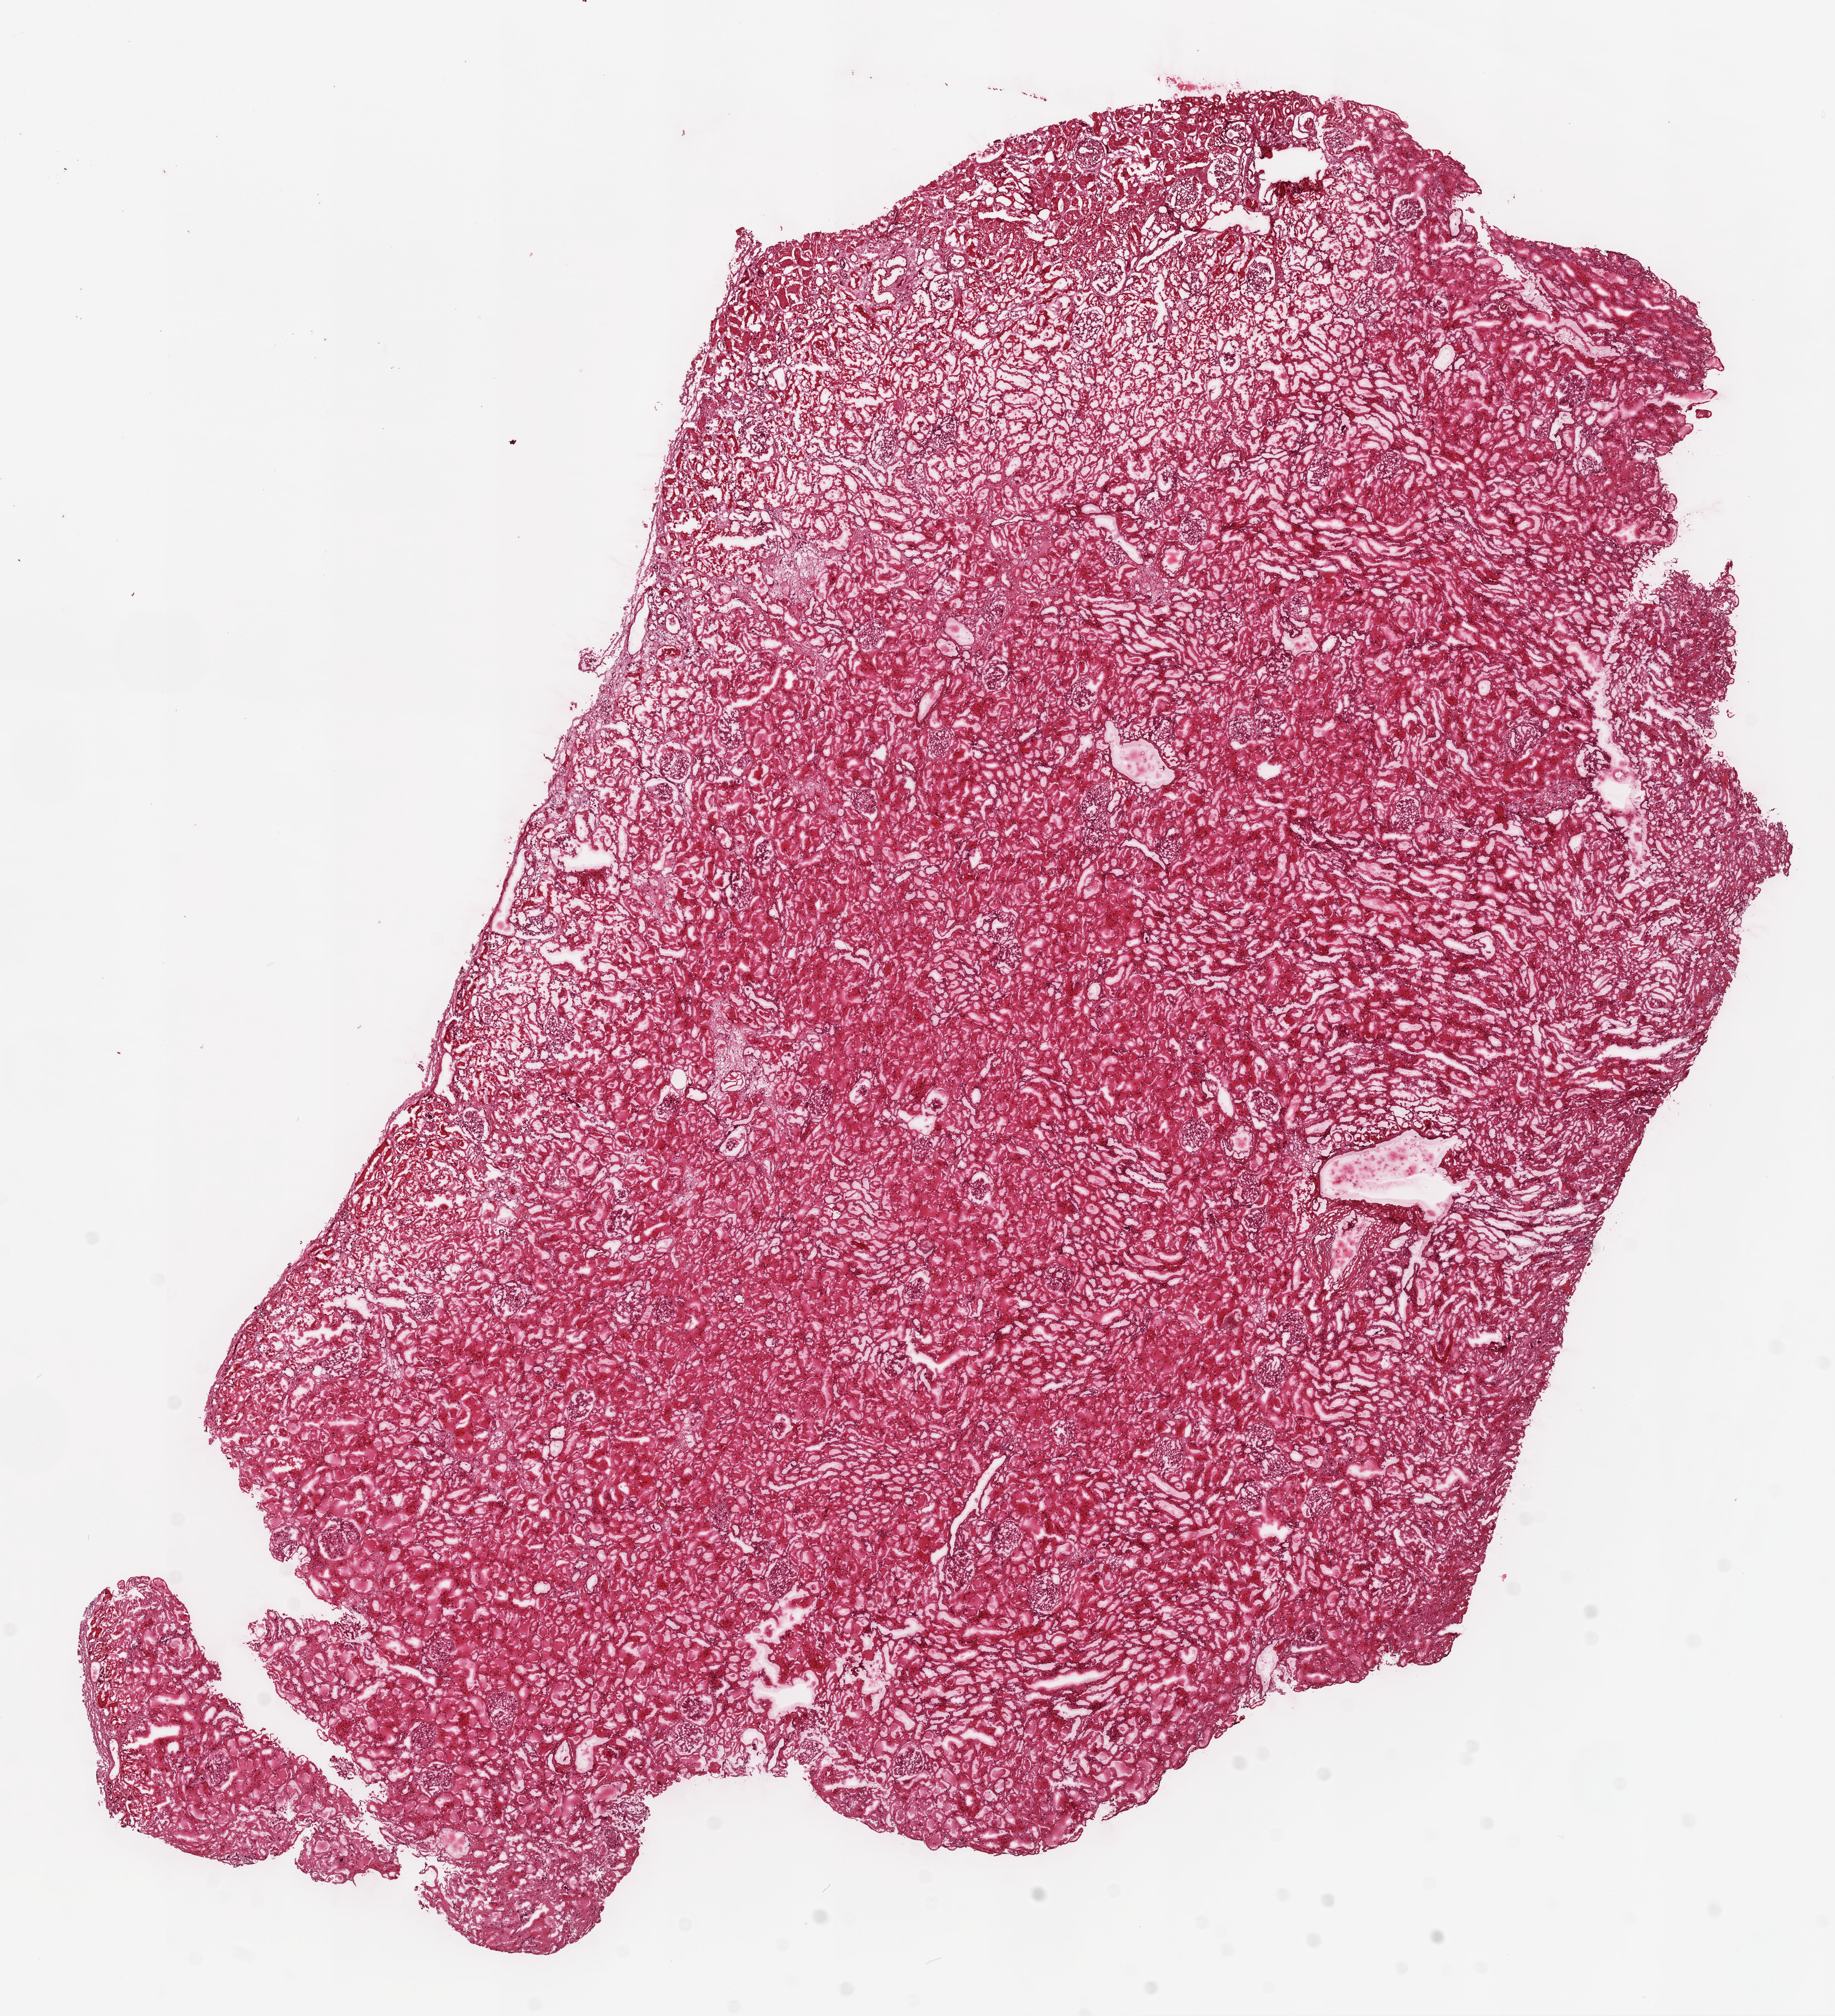
Digitized Hematoxylin and eosin (H&E) stained tissue section (whole slide) — a low-resolution overview of the entire scanned area, about 11.0 x 12.1 mm (acquisition: 20x scan); frozen section from the top of the tissue portion; solid tissue normal (non-tumour tissue) sample from the kidney. Patient: male, age at initial diagnosis 74 years.
This section: solid tissue normal (non-tumour) sample from the same patient. Patient diagnosis: Clear cell adenocarcinoma, NOS.